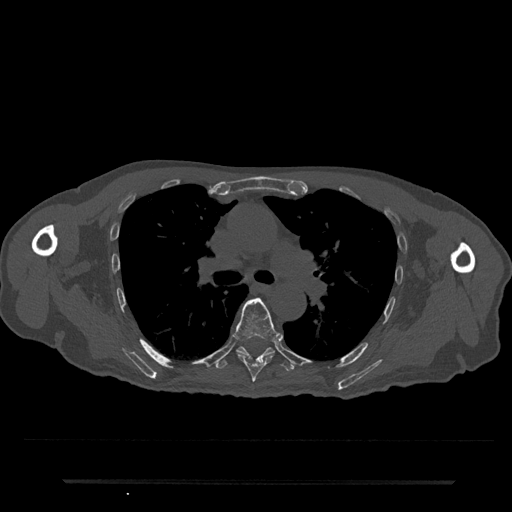
CT including the spine, one axial slice; slice 514 of 797 in the series (ordered by position); bone window (W 1800 / L 400 HU); 0.5 mm slice thickness; 512 × 512 image matrix, field of view 427 × 427 mm. Patient: male, 74 years. From the clinical record (not read from this slice): primary cancer: prostate.
Outlined on this slice (semi-automatic segmentation, software-assisted and operator-edited):
- T6 vertebra: bounding box (x1, y1, x2, y2) in pixels: (234, 298, 280, 382)
- T7 vertebra: (216, 347, 294, 371)